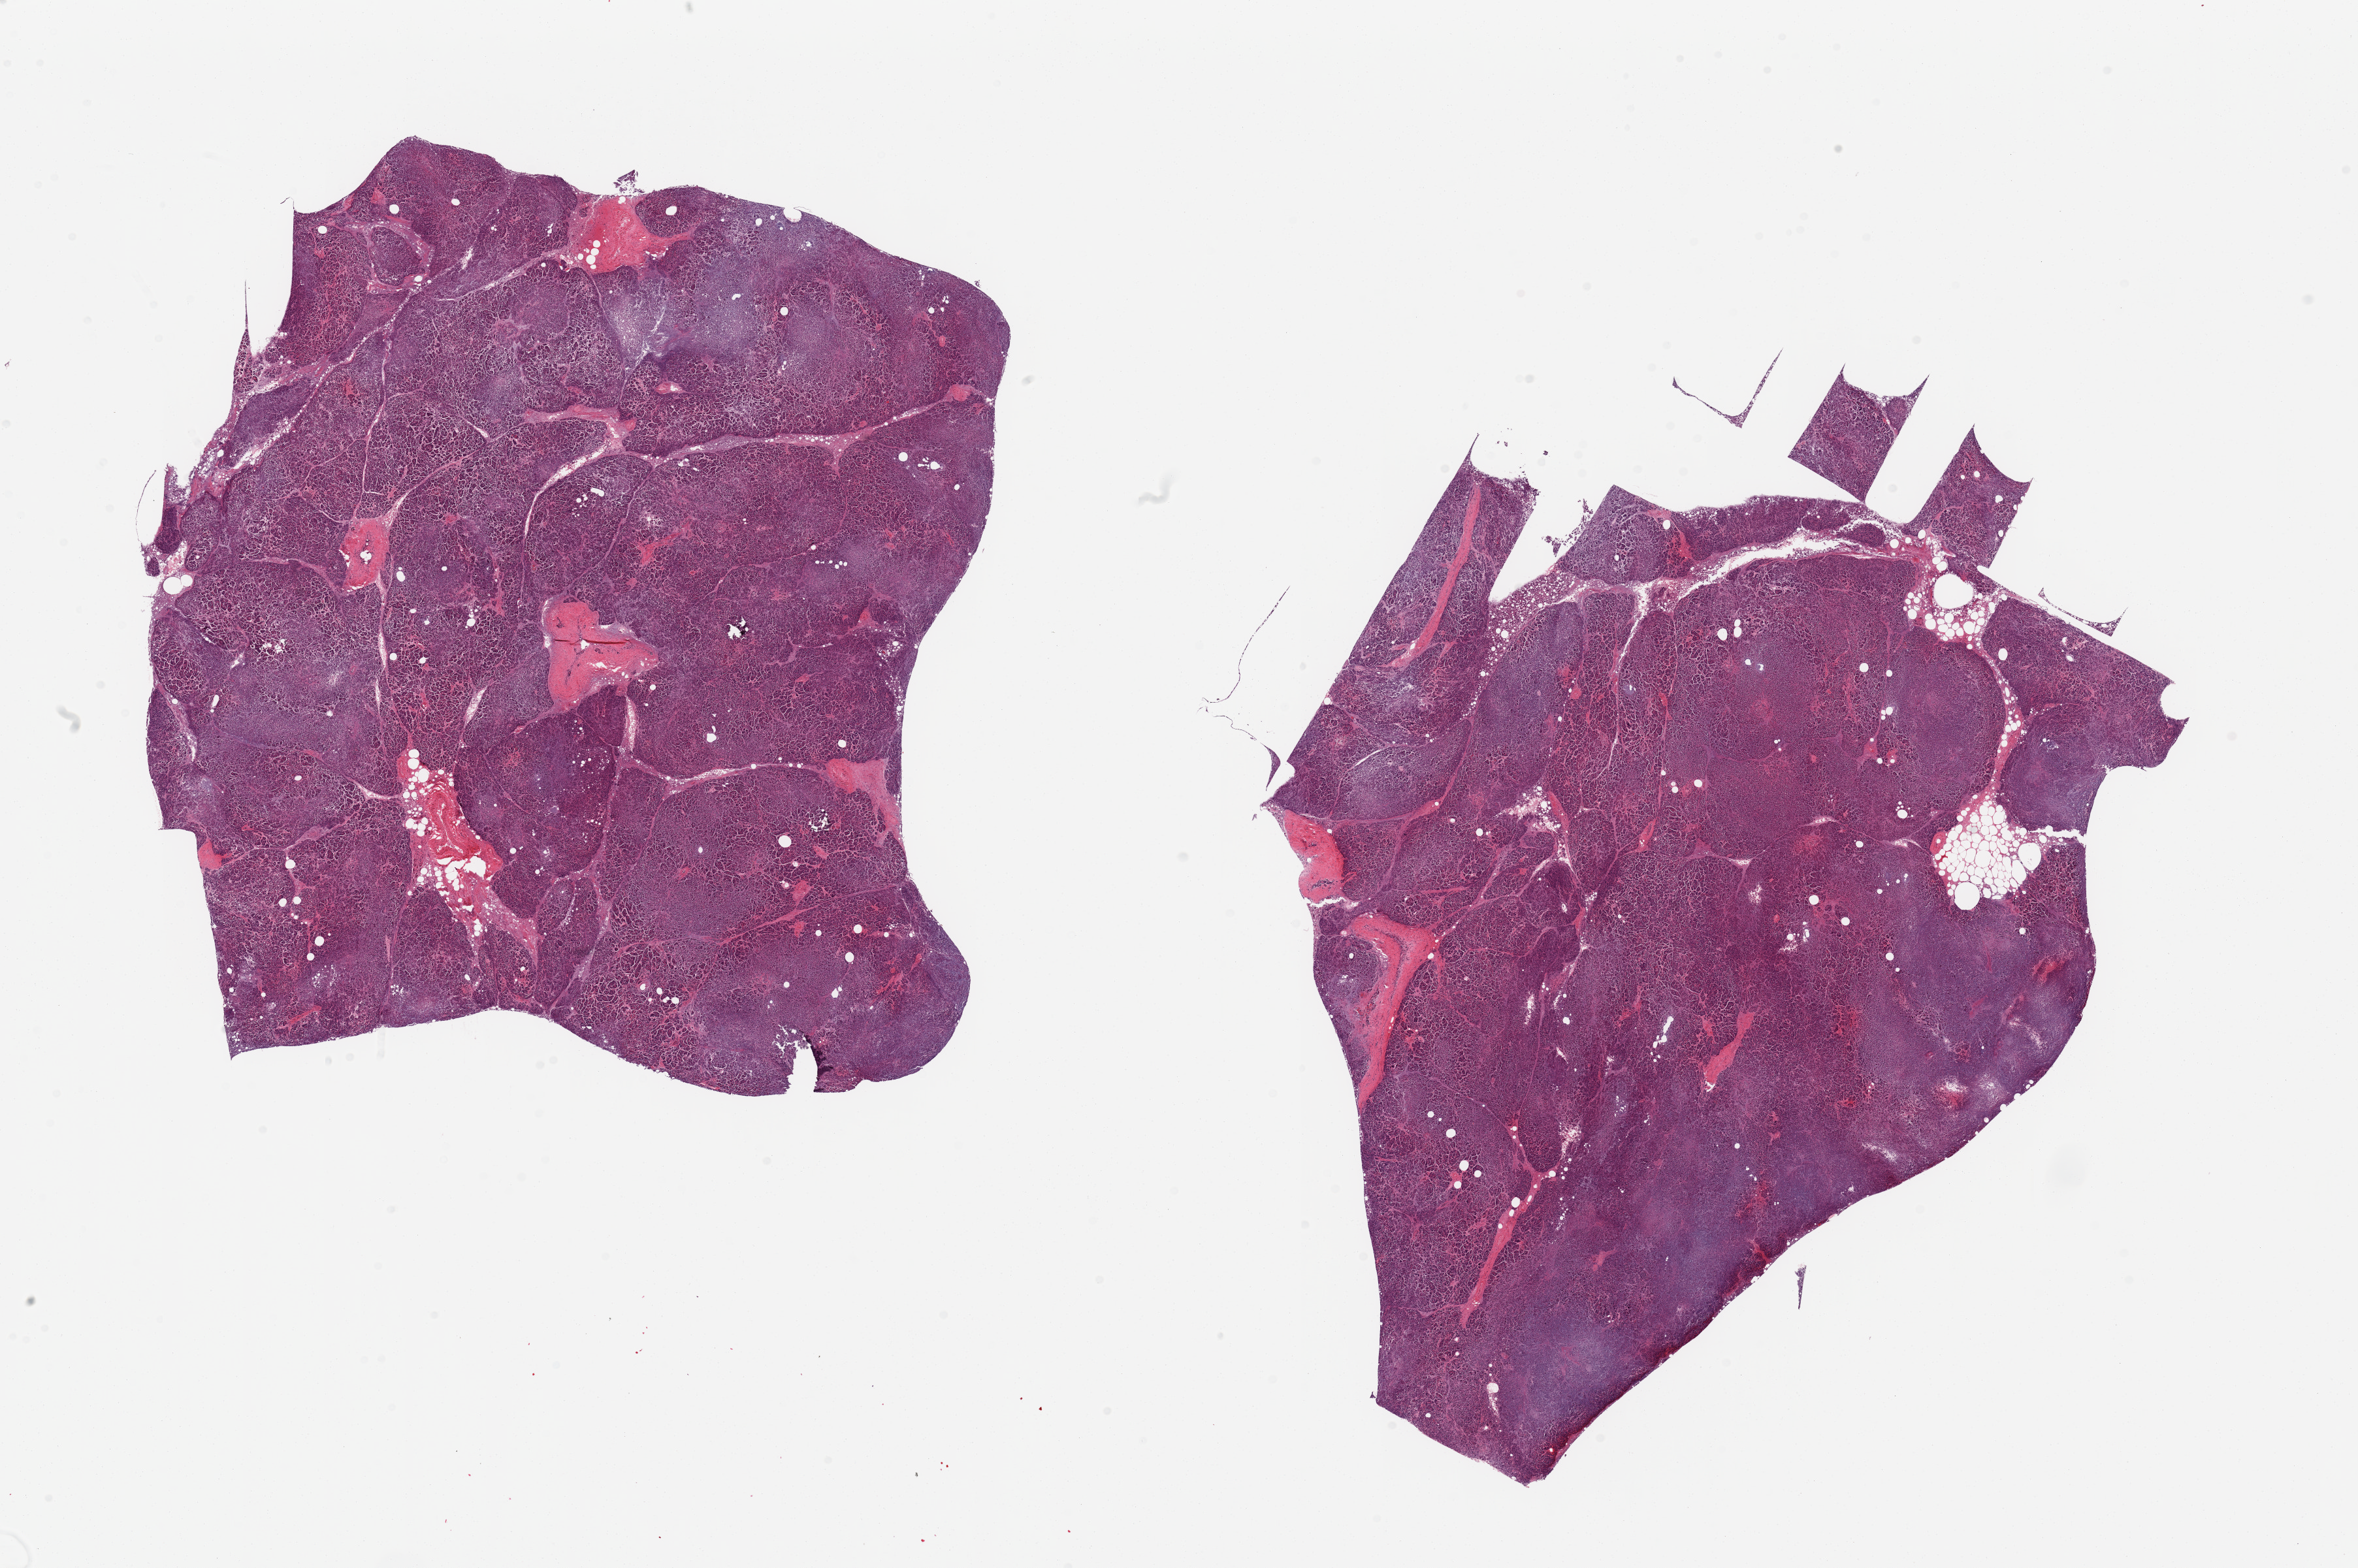
Whole-slide image, hematoxylin and eosin (H&E) stain, a low-resolution overview of the entire scanned area, about 28.5 x 19.0 mm (acquisition: 20x scan); PAXgene-fixed paraffin-embedded (PFPE) section; section of pancreas (target tissue); tissue donor sample. Donor: male.
Reviewer comment on this tissue sample: 2 pieces; <10% internal fat.